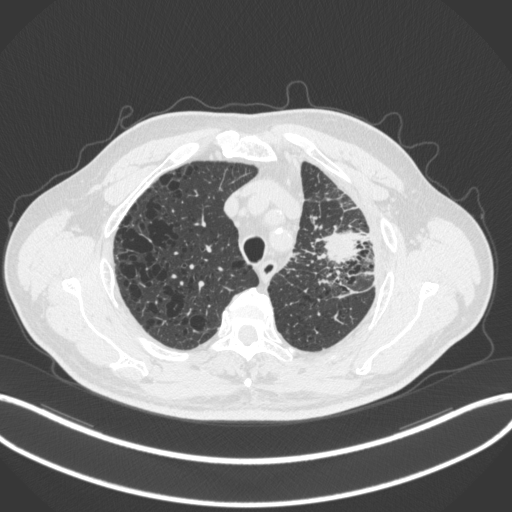
Chest CT, one axial slice. Position 244 of 286 along the scan axis. Lung window (W 1500 / L -600 HU). 512 × 512 image matrix, field of view 400 × 400 mm. Male patient, age 68 years. From the clinical record (not read from this slice): clinical TNM (as recorded): T3 N3 M1.
Outlined on this slice (bounding box drawn by a radiologist):
- lung tumour (recorded histology: adenocarcinoma): bounding box <314,221,362,268> (left, top, right, bottom; pixels)